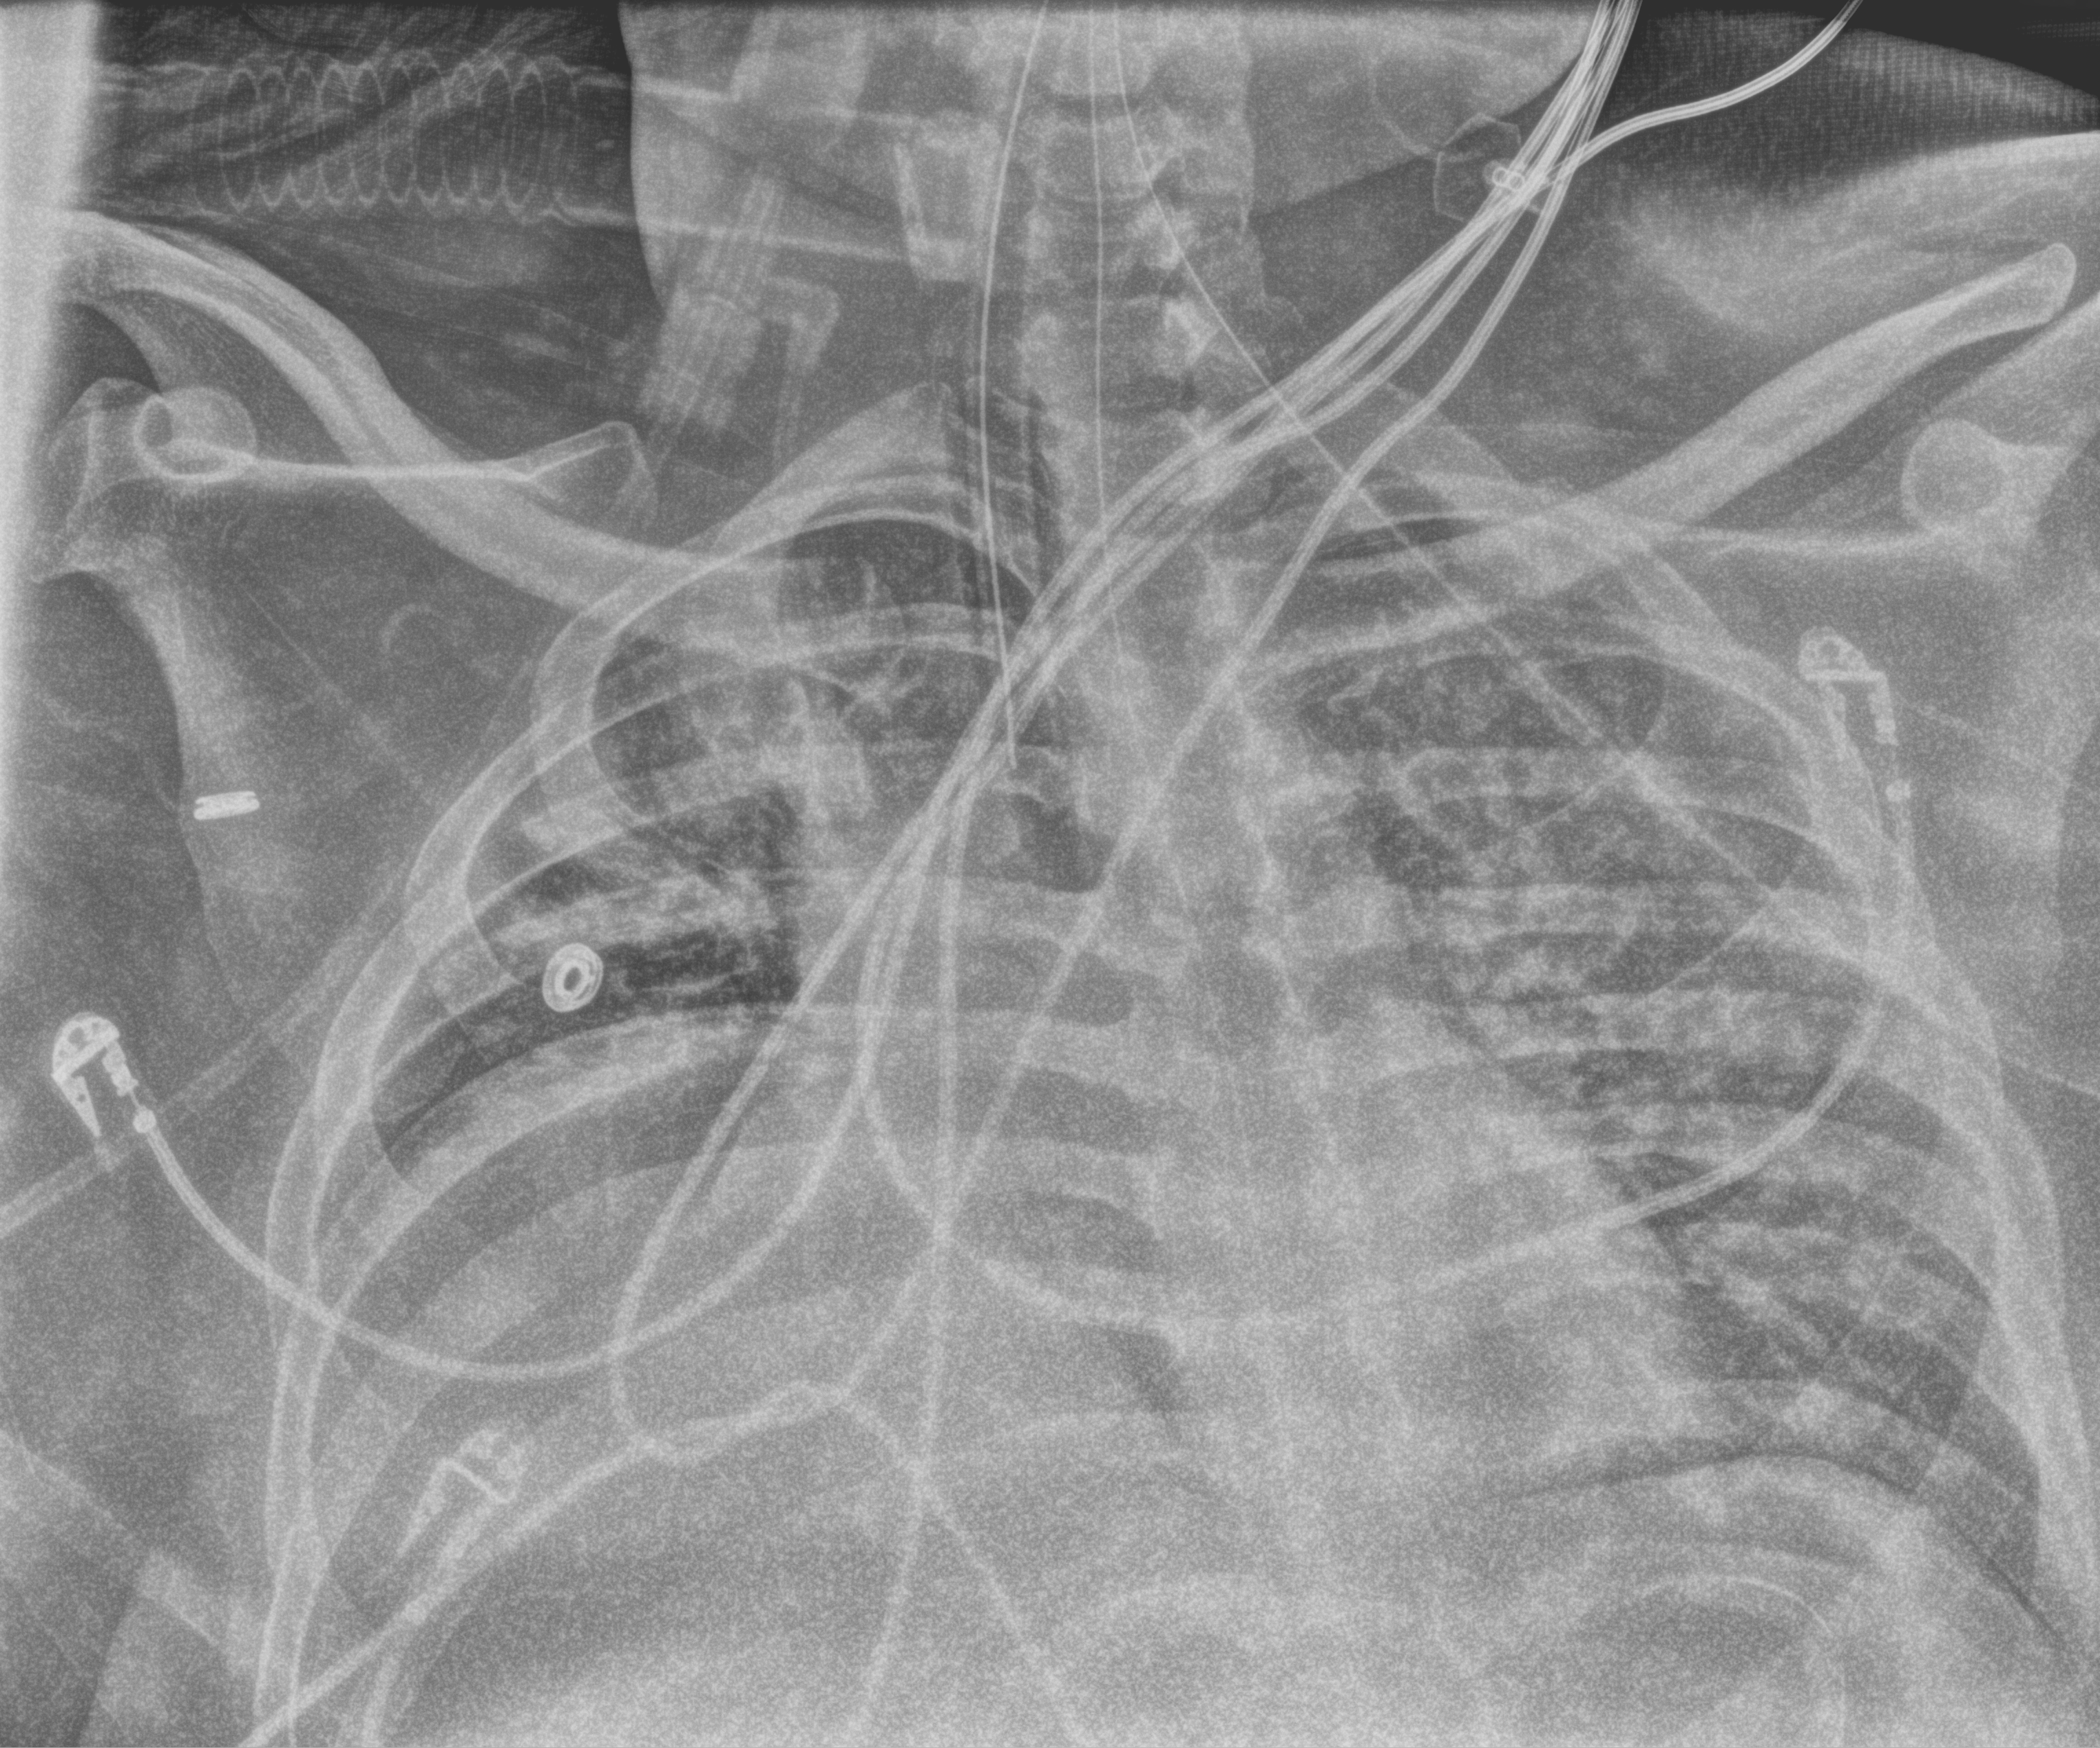
Chest X-ray (portable); anteroposterior (AP) projection. Male patient hospitalised with COVID-19, age 18–59 years.
Hospital-stay facts (about this admission, not read from this image; timing relative to this image not recorded):
- admitted to intensive care during this hospital stay: yes
- length of hospital stay: 69 days
- other chronic lung disease (admission record): yes